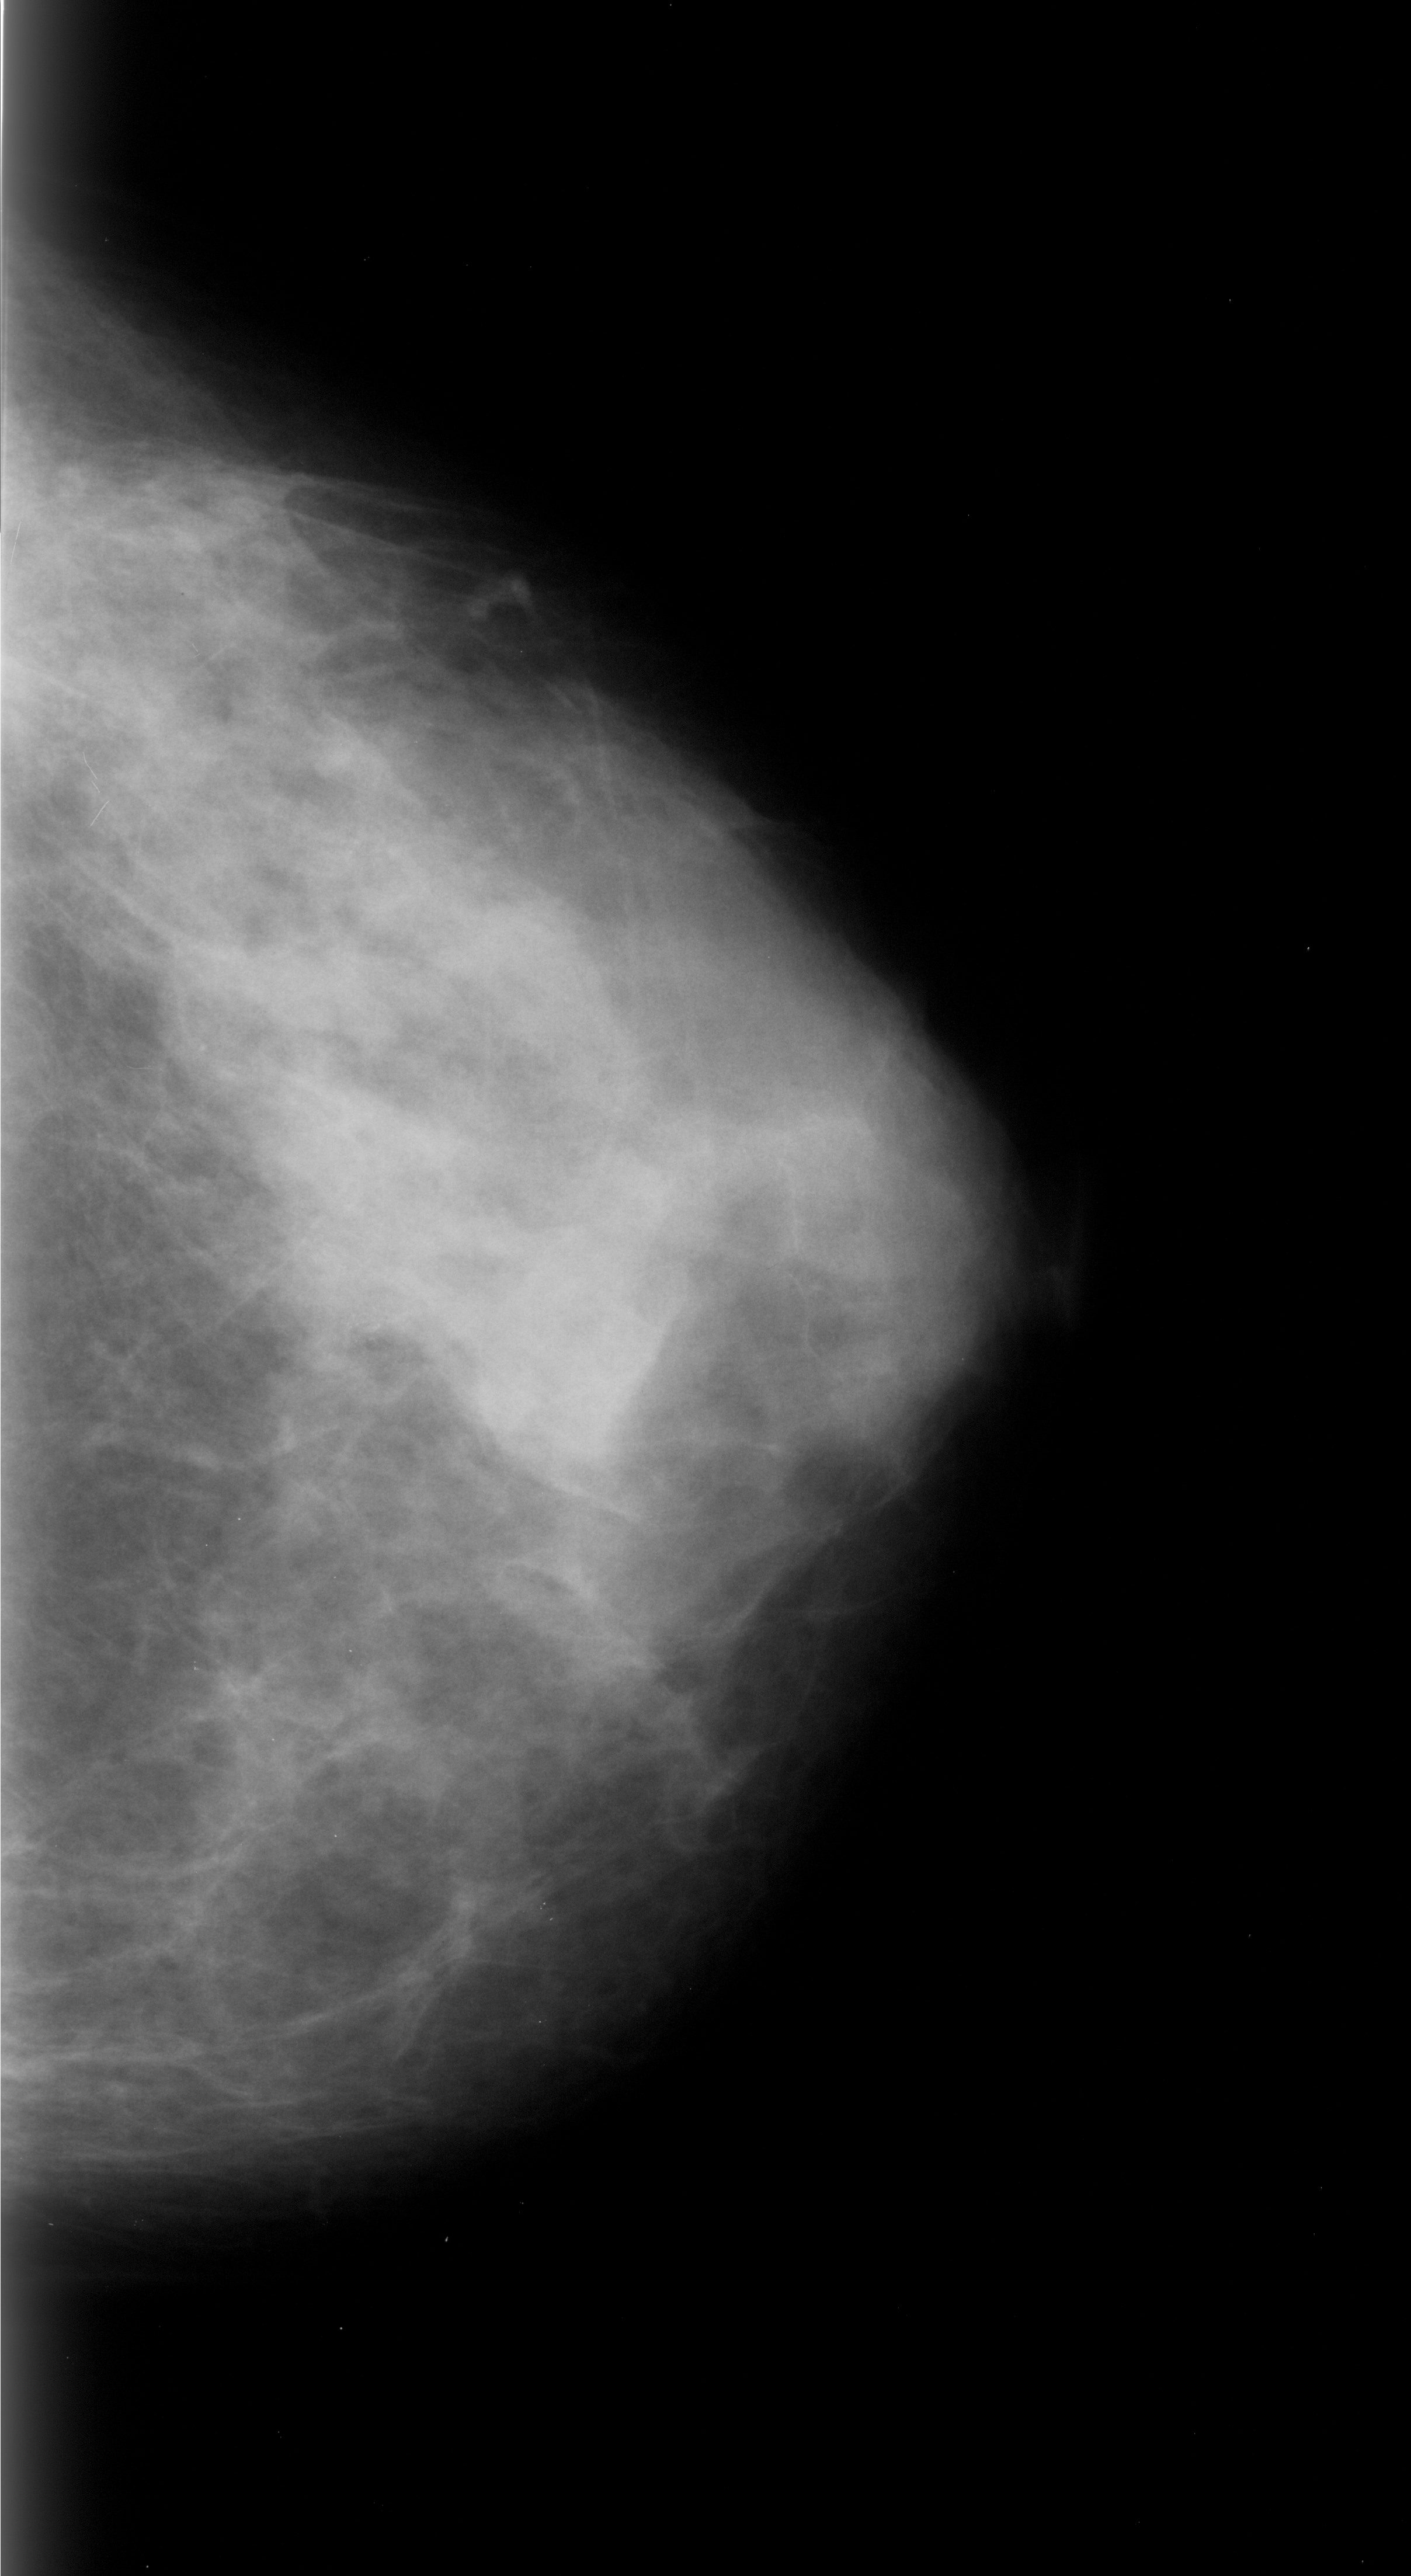
Mammogram (digitized film); right breast; CC view; BI-RADS breast density category 4 (scale 1–4); 1411 × 2576 image matrix.
Expert-marked regions of interest on this film, with their recorded descriptors:
- calcifications, morphology pleomorphic, distribution clustered; BI-RADS assessment category 4; subtlety rating 1 on a 1 (subtle) to 5 (obvious) scale; pathology (as recorded): malignant: bounding box (x1, y1, x2, y2) in pixels: (310, 1288, 426, 1372)